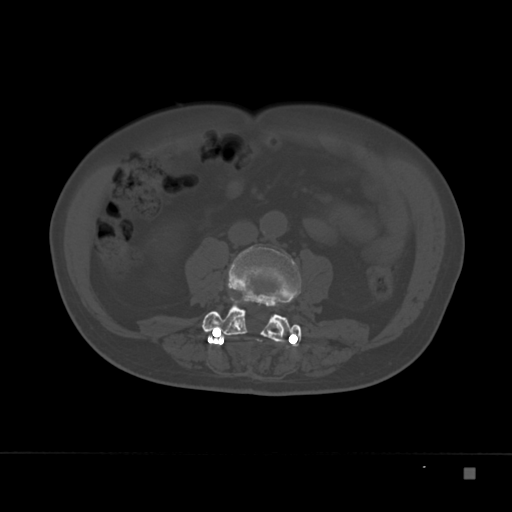
CT including the spine, one axial slice. Slice 57 of 332 in the series (ordered by position). Bone window (W 1800 / L 400 HU). 512 × 512 image matrix, field of view 389 × 389 mm. Patient: male, 72 years. From the clinical record (not read from this slice): primary cancer: skeletal.
Structures marked on this image (semi-automatically segmented with operator editing):
- L3 vertebra: box from (x=205, y=247) to (x=301, y=332) px
- L4 vertebra: (x=202, y=296)–(x=302, y=347)